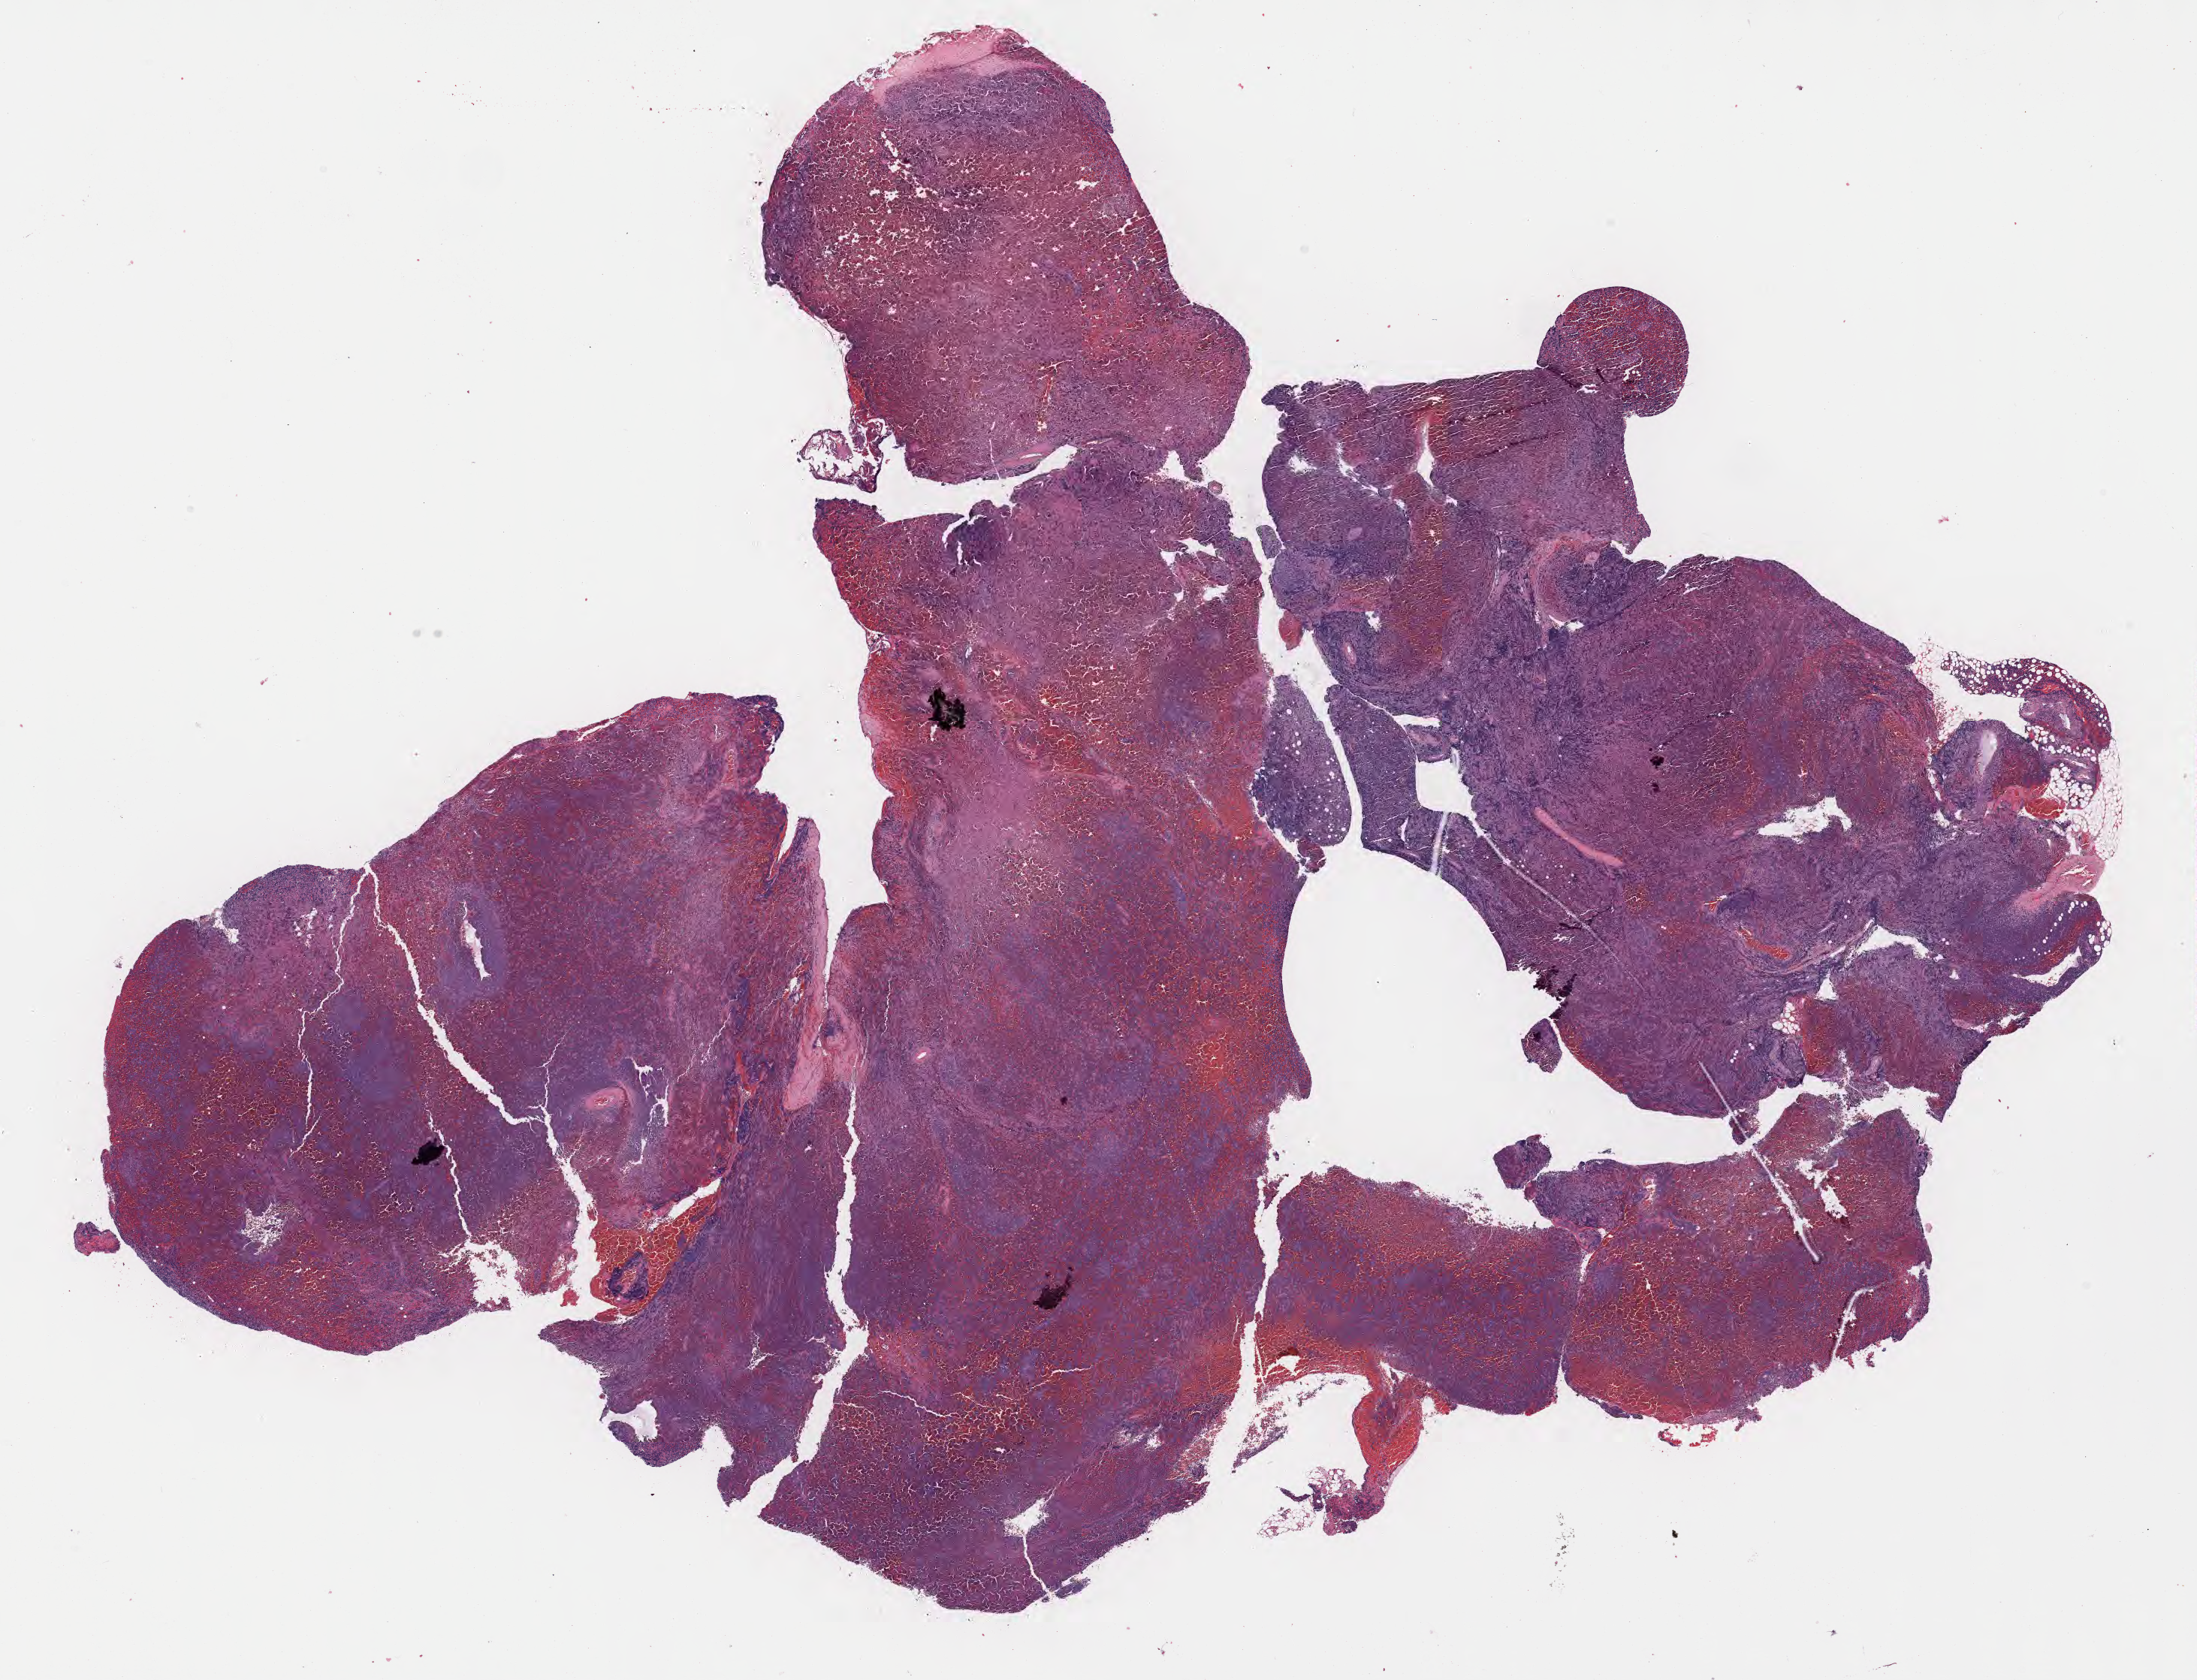
Whole-slide image, haematoxylin and eosin stain — whole scanned area (about 23.7 x 18.1 mm) shown as a low-resolution overview; specimen: tumor tissue; site: soft tissue of abdomen. Female patient; age at initial diagnosis 8 years.
- histologic diagnosis: Burkitt lymphoma, NOS